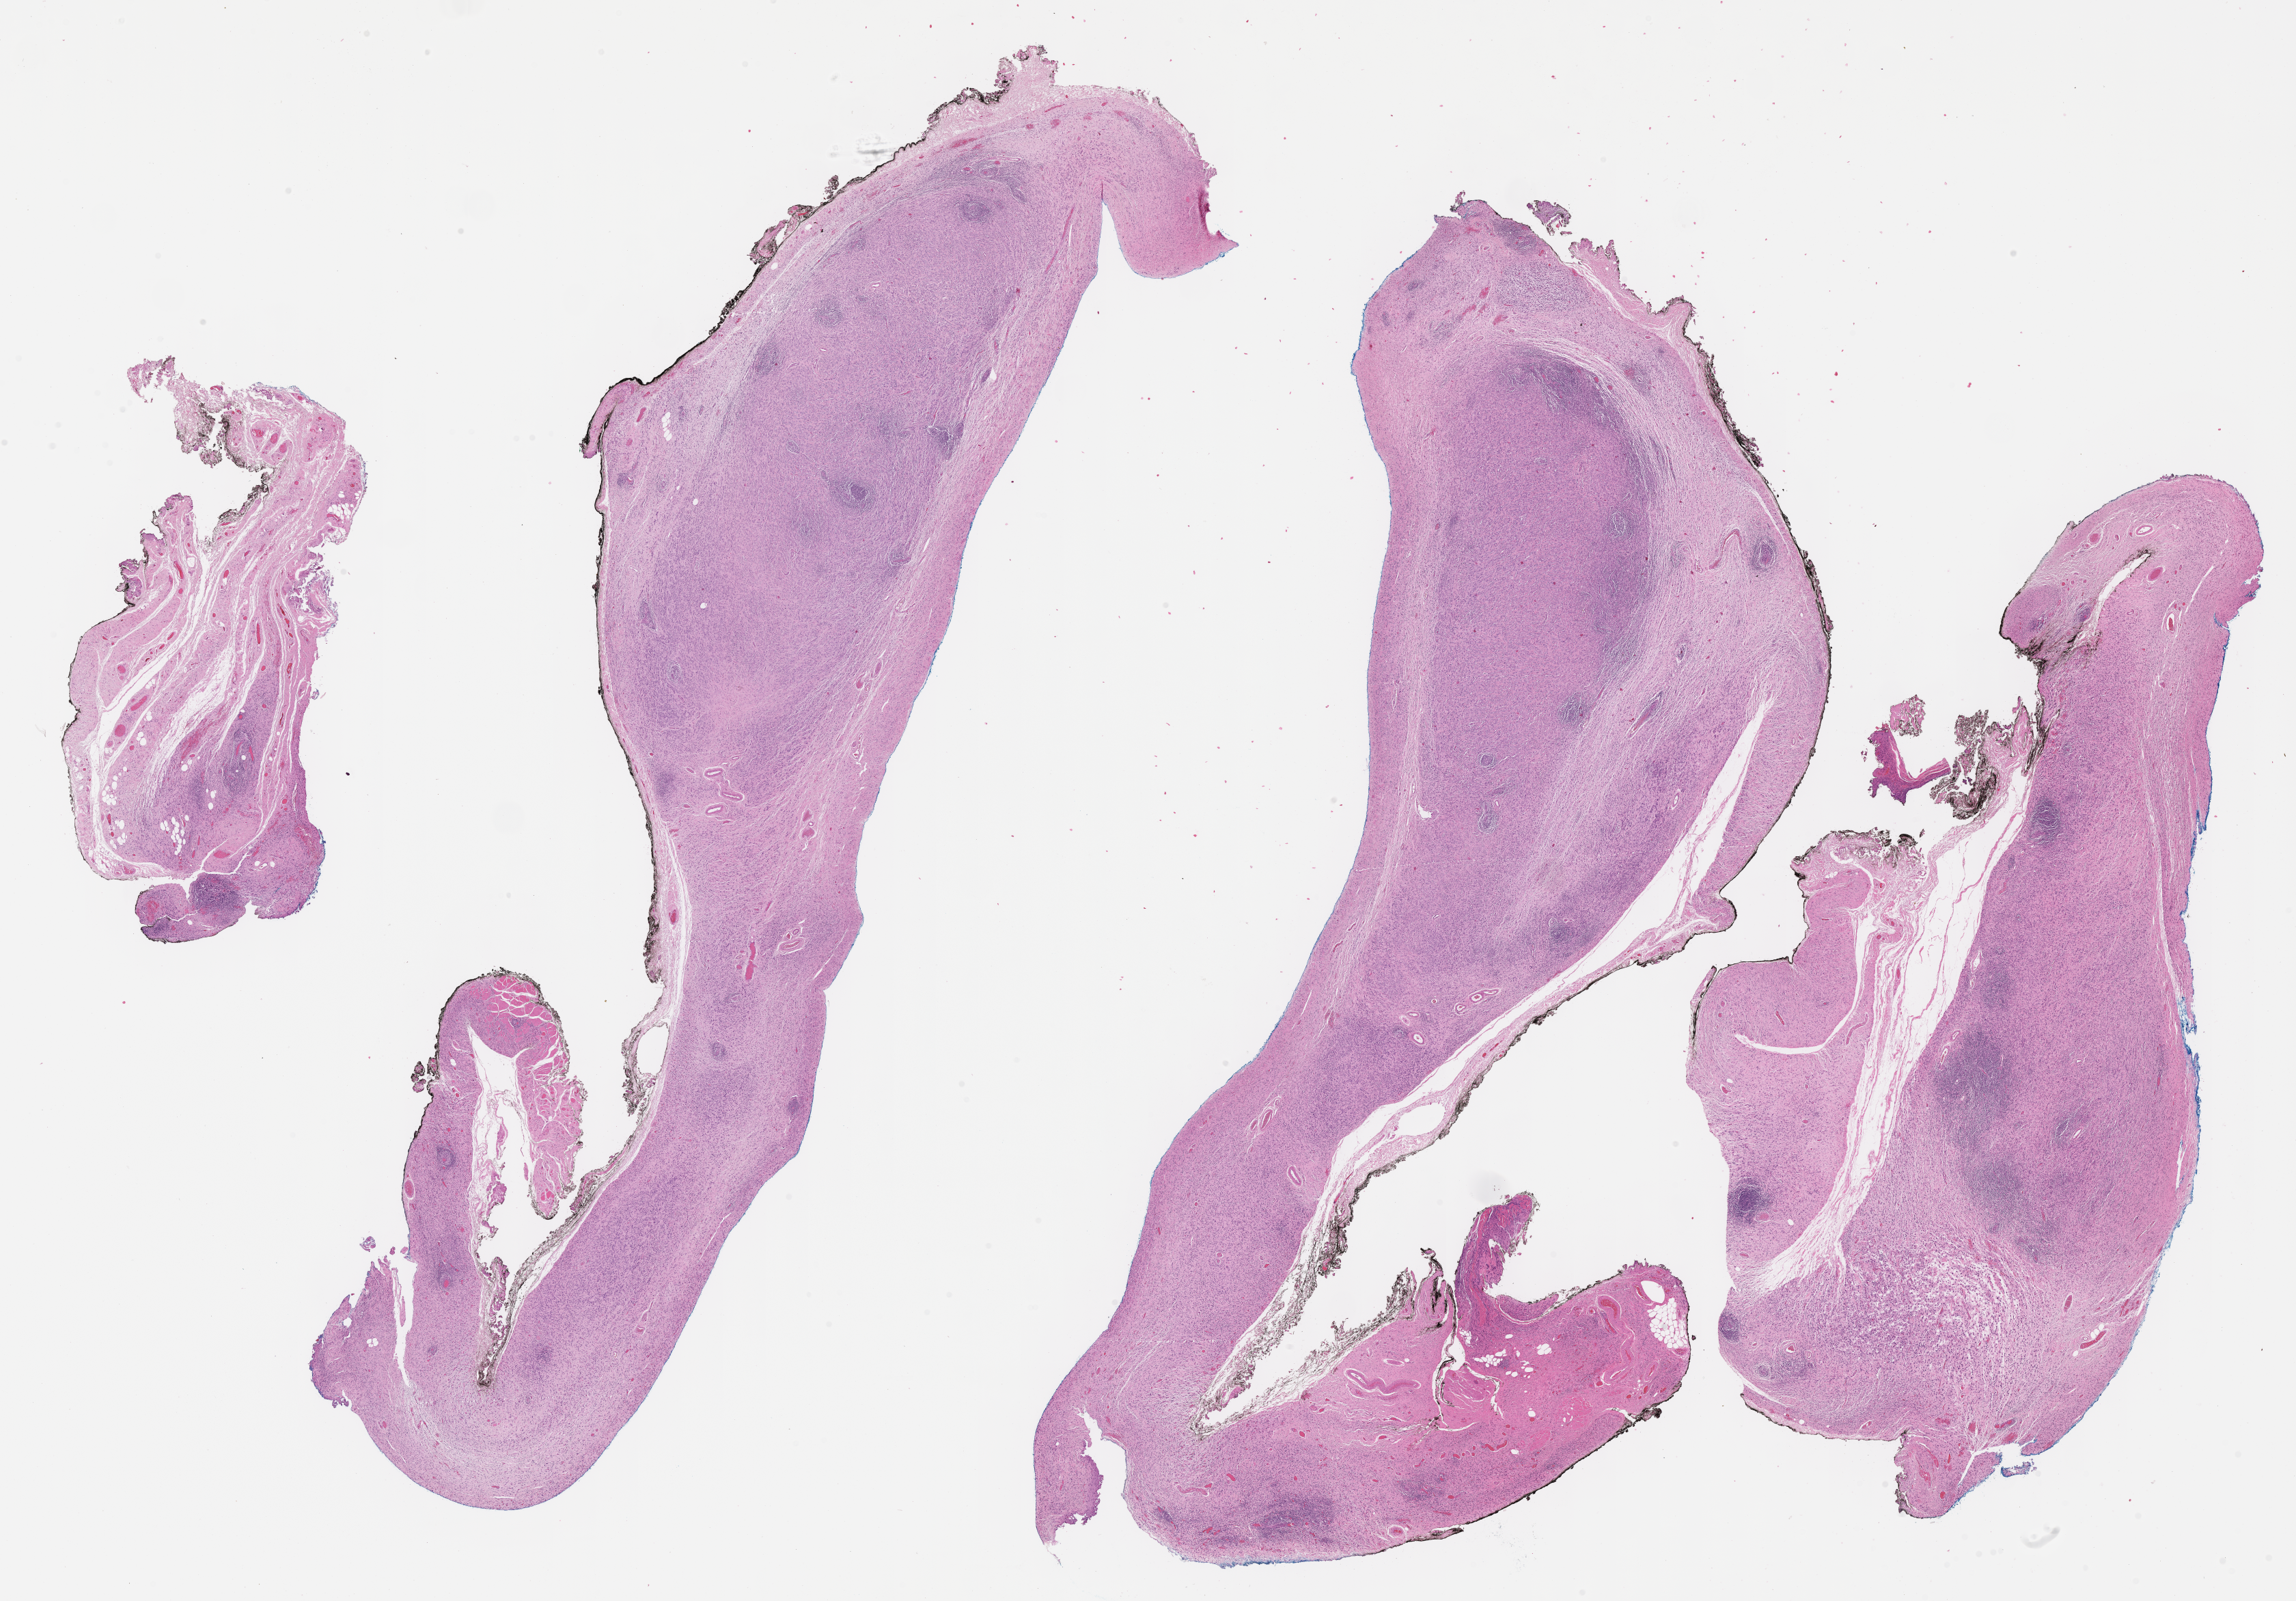
Digitized hematoxylin and eosin (H&E)-stained section of tumor tissue — shown as a low-resolution overview of the whole scanned area (about 27.2 x 18.9 mm); FFPE section; site: testicle, left. Male patient, age at diagnosis 7.3 years.
• metastatic status at presentation (as recorded): non-metastatic (confirmed)
• stage (as recorded): 1
• primary site (case record): testis-paratesticular
• diagnosis: rhabdomyosarcoma; histological classification: embryonal rhabdomyosarcoma